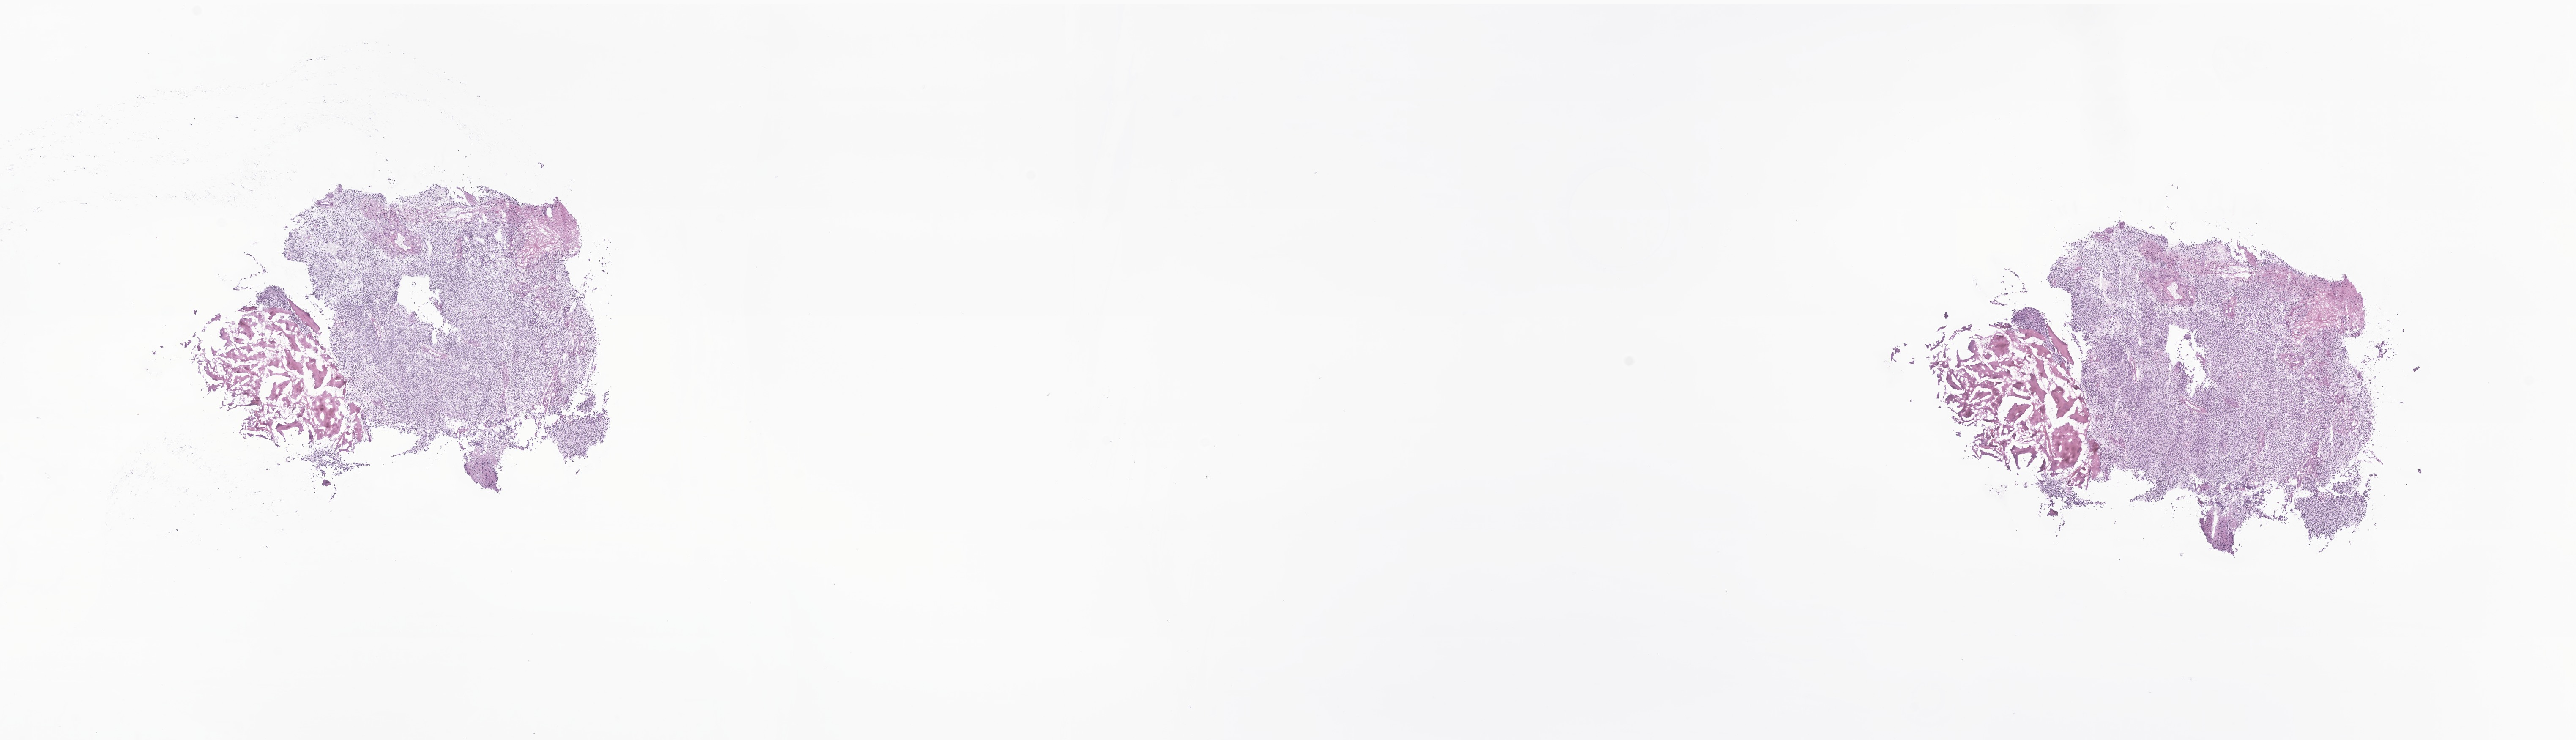
Hematoxylin and eosin (H&E) whole-slide image of tumor tissue from the brain — low-resolution overview of the scanned area, about 25.7 x 7.4 mm. Frozen section. Patient male; age 76 months (6 years 4 months).
- recorded diagnosis: Ependymoma, NOS